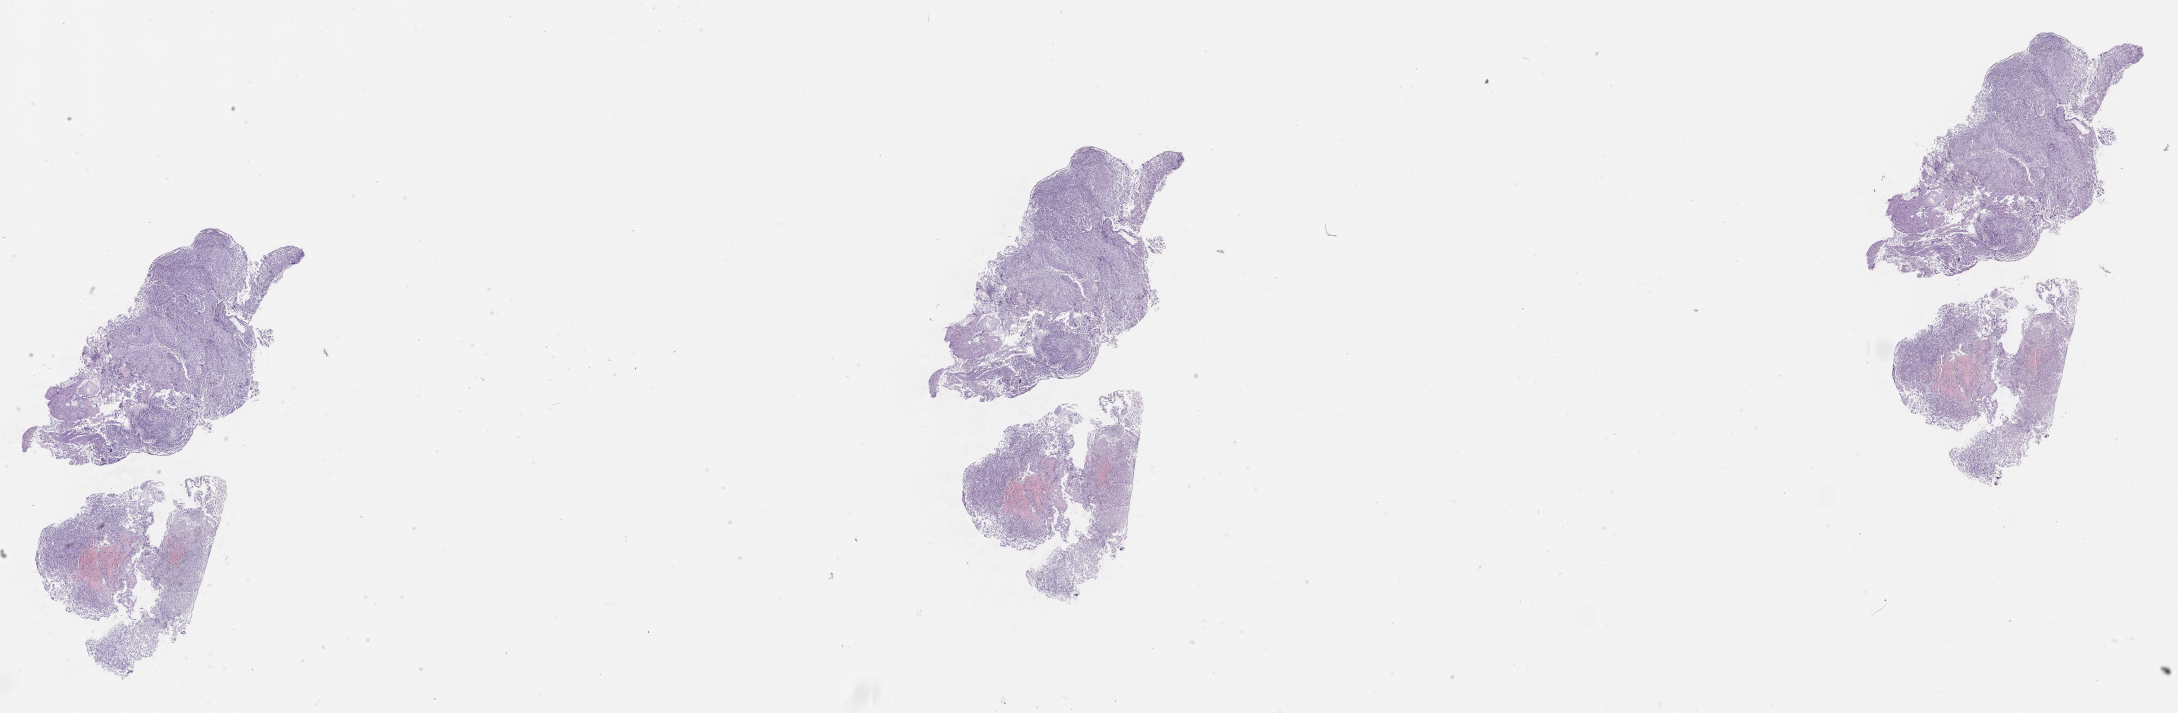
Hematoxylin and eosin (H&E) stained whole-slide image, a low-resolution overview of the entire scanned area, about 35.1 x 11.5 mm; tumour tissue sample, sampled site: brain. Patient: female, age 81 years. Slide review estimates, as recorded: tumour nuclei 80%, necrosis 15%.
Diagnosis: Glioblastoma. Primary tumour site (as recorded): parietal lobe.